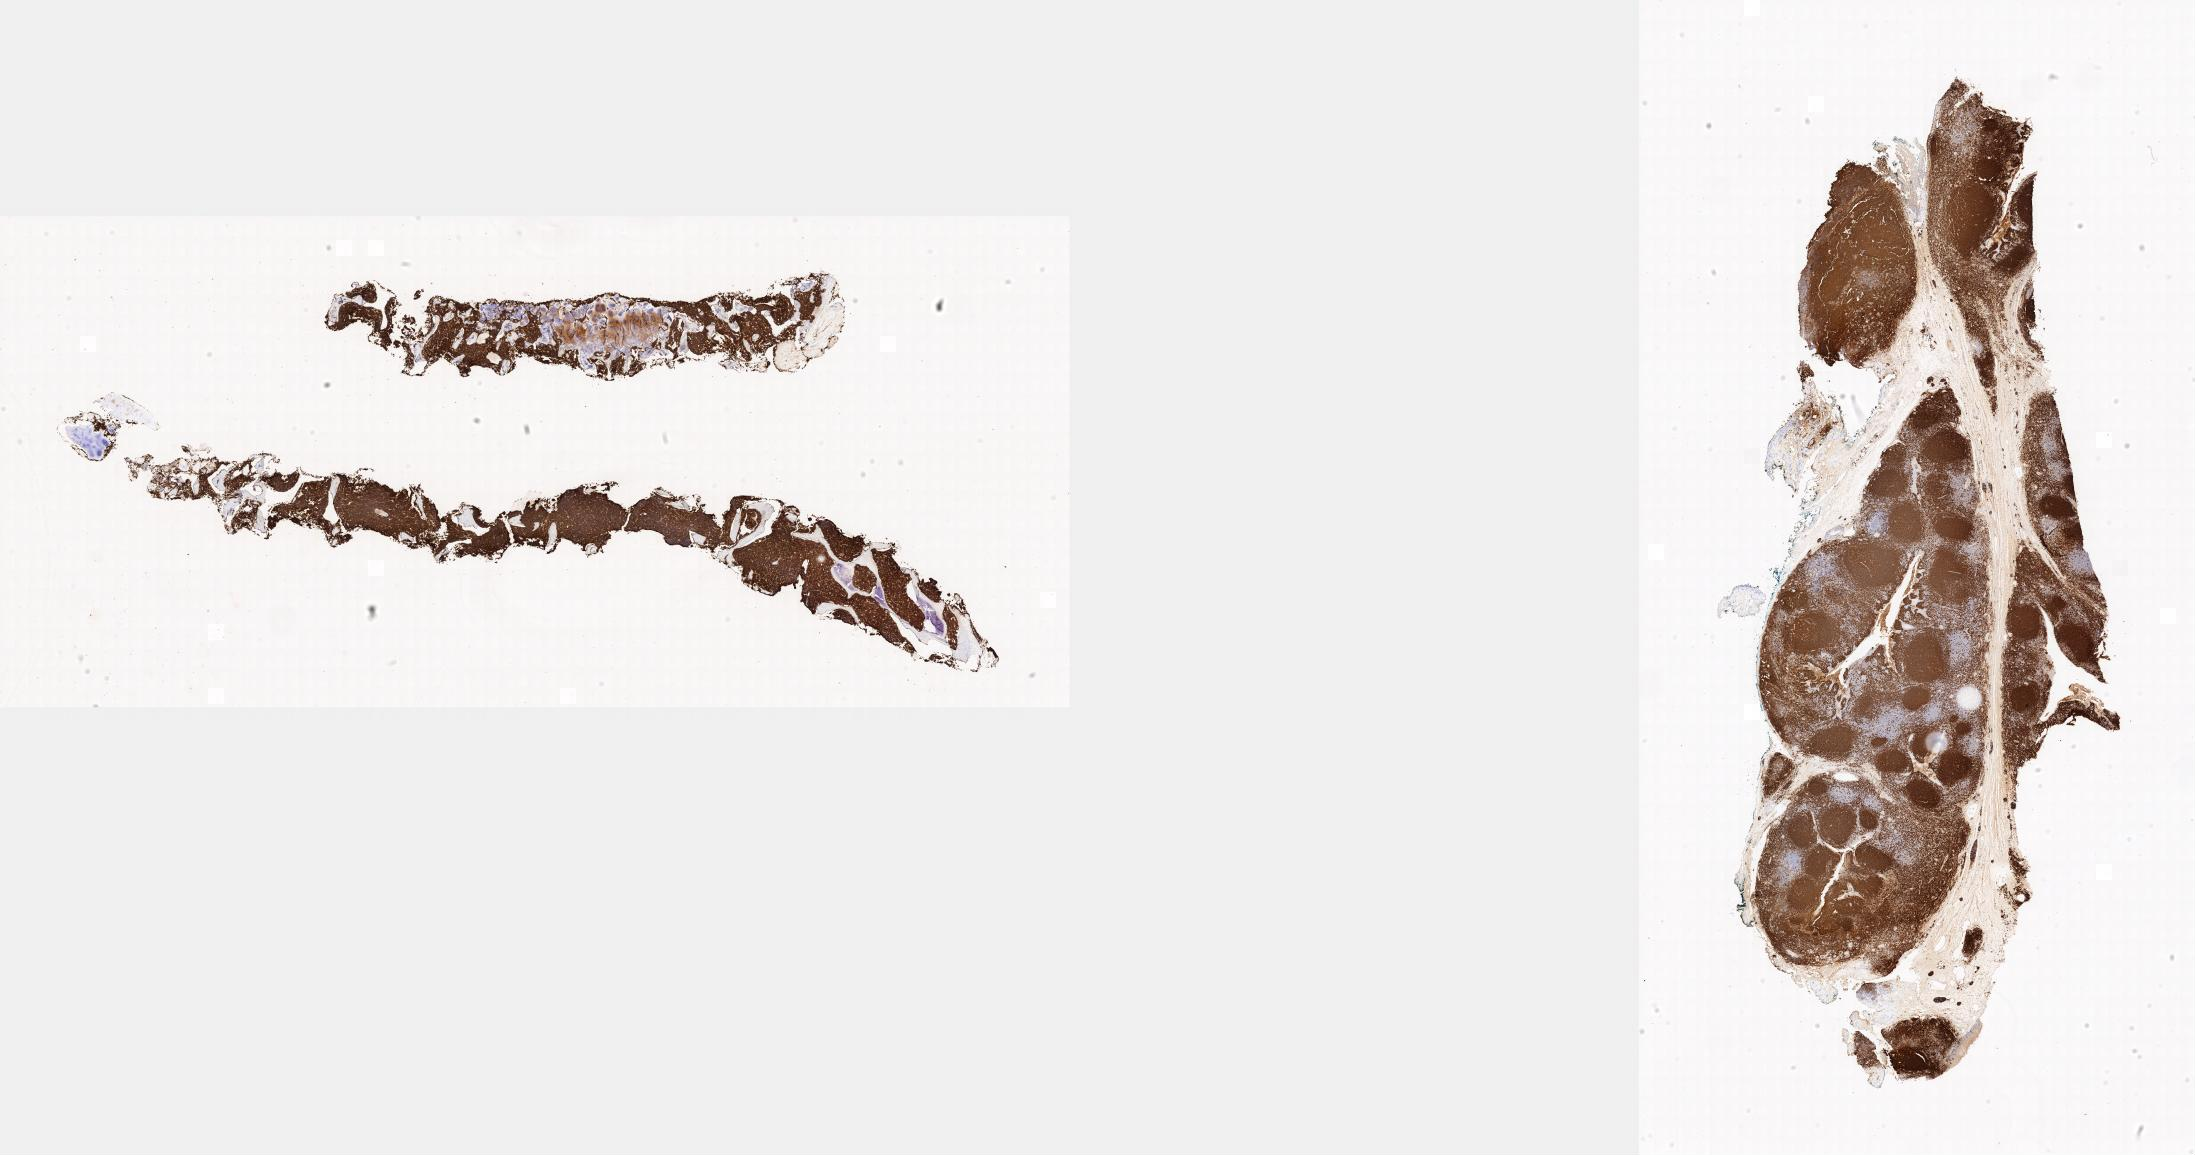
Immunohistochemistry (IHC) whole-slide image stained for CD20, a low-resolution overview of the entire scanned area, specimen: tumor tissue, site: bone marrow. Male patient, age 11 years.
- histologic diagnosis: Burkitt lymphoma, NOS